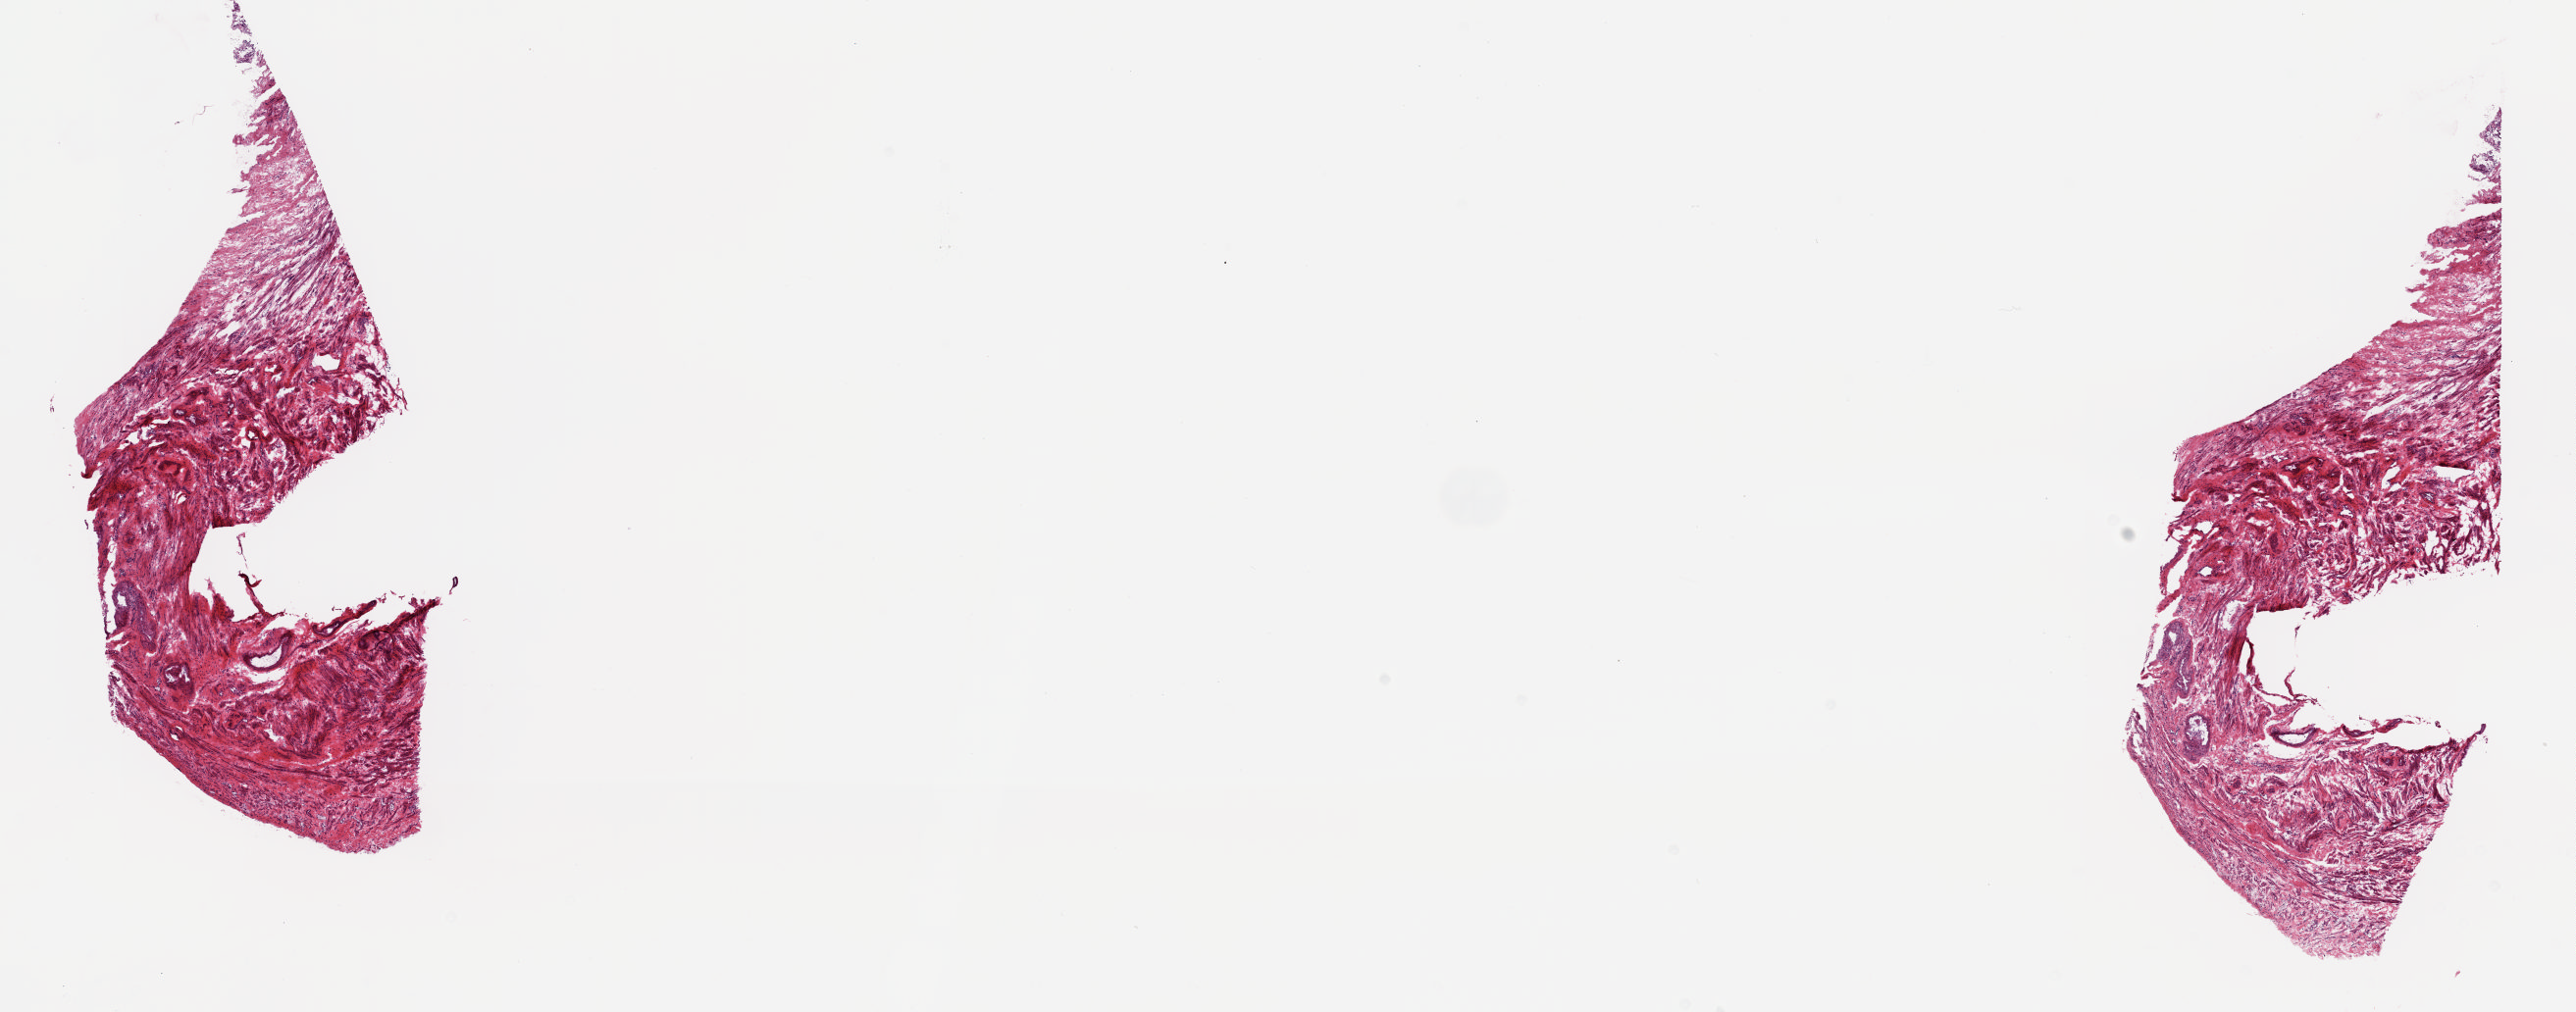
H&E-stained whole-slide image — whole scanned area (about 20.8 x 8.2 mm, from a 20x scan) shown as a low-resolution overview. Frozen section from the top of the tissue portion. Solid tissue normal (non-tumour tissue) sample from the uterus. Patient: female, age at initial diagnosis 68 years. Composition of this section per pathologist review: tumour cells 0%, tumour nuclei 0%, normal cells 100%, stromal cells 0%, necrosis 0%. Infiltration values recorded for this section: lymphocyte infiltration 40%, monocyte infiltration 0%, neutrophil infiltration 10%.
This section: solid tissue normal (non-tumour) sample from the same patient. Patient diagnosis: Endometrioid adenocarcinoma, NOS.